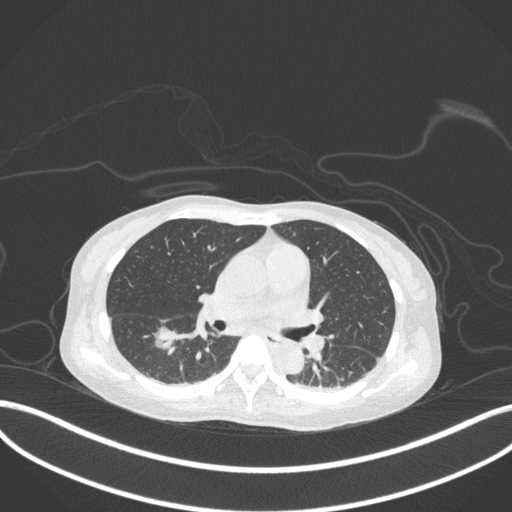
Chest CT, one axial slice; position 170 of 260 along the scan axis; reconstruction kernel B31f; 120 kVp; lung window (W 1500 / L -600 HU); 1 mm slice thickness; 512 × 512 image matrix, field of view 400 × 400 mm. Female patient, age 44 years. From the clinical record (not read from this slice): clinical TNM (as recorded): T1c N0 M0.
Annotated regions visible in this slice (bounding box drawn by a radiologist):
- lung tumour (recorded histology: adenocarcinoma): box from (x=150, y=318) to (x=179, y=353) px